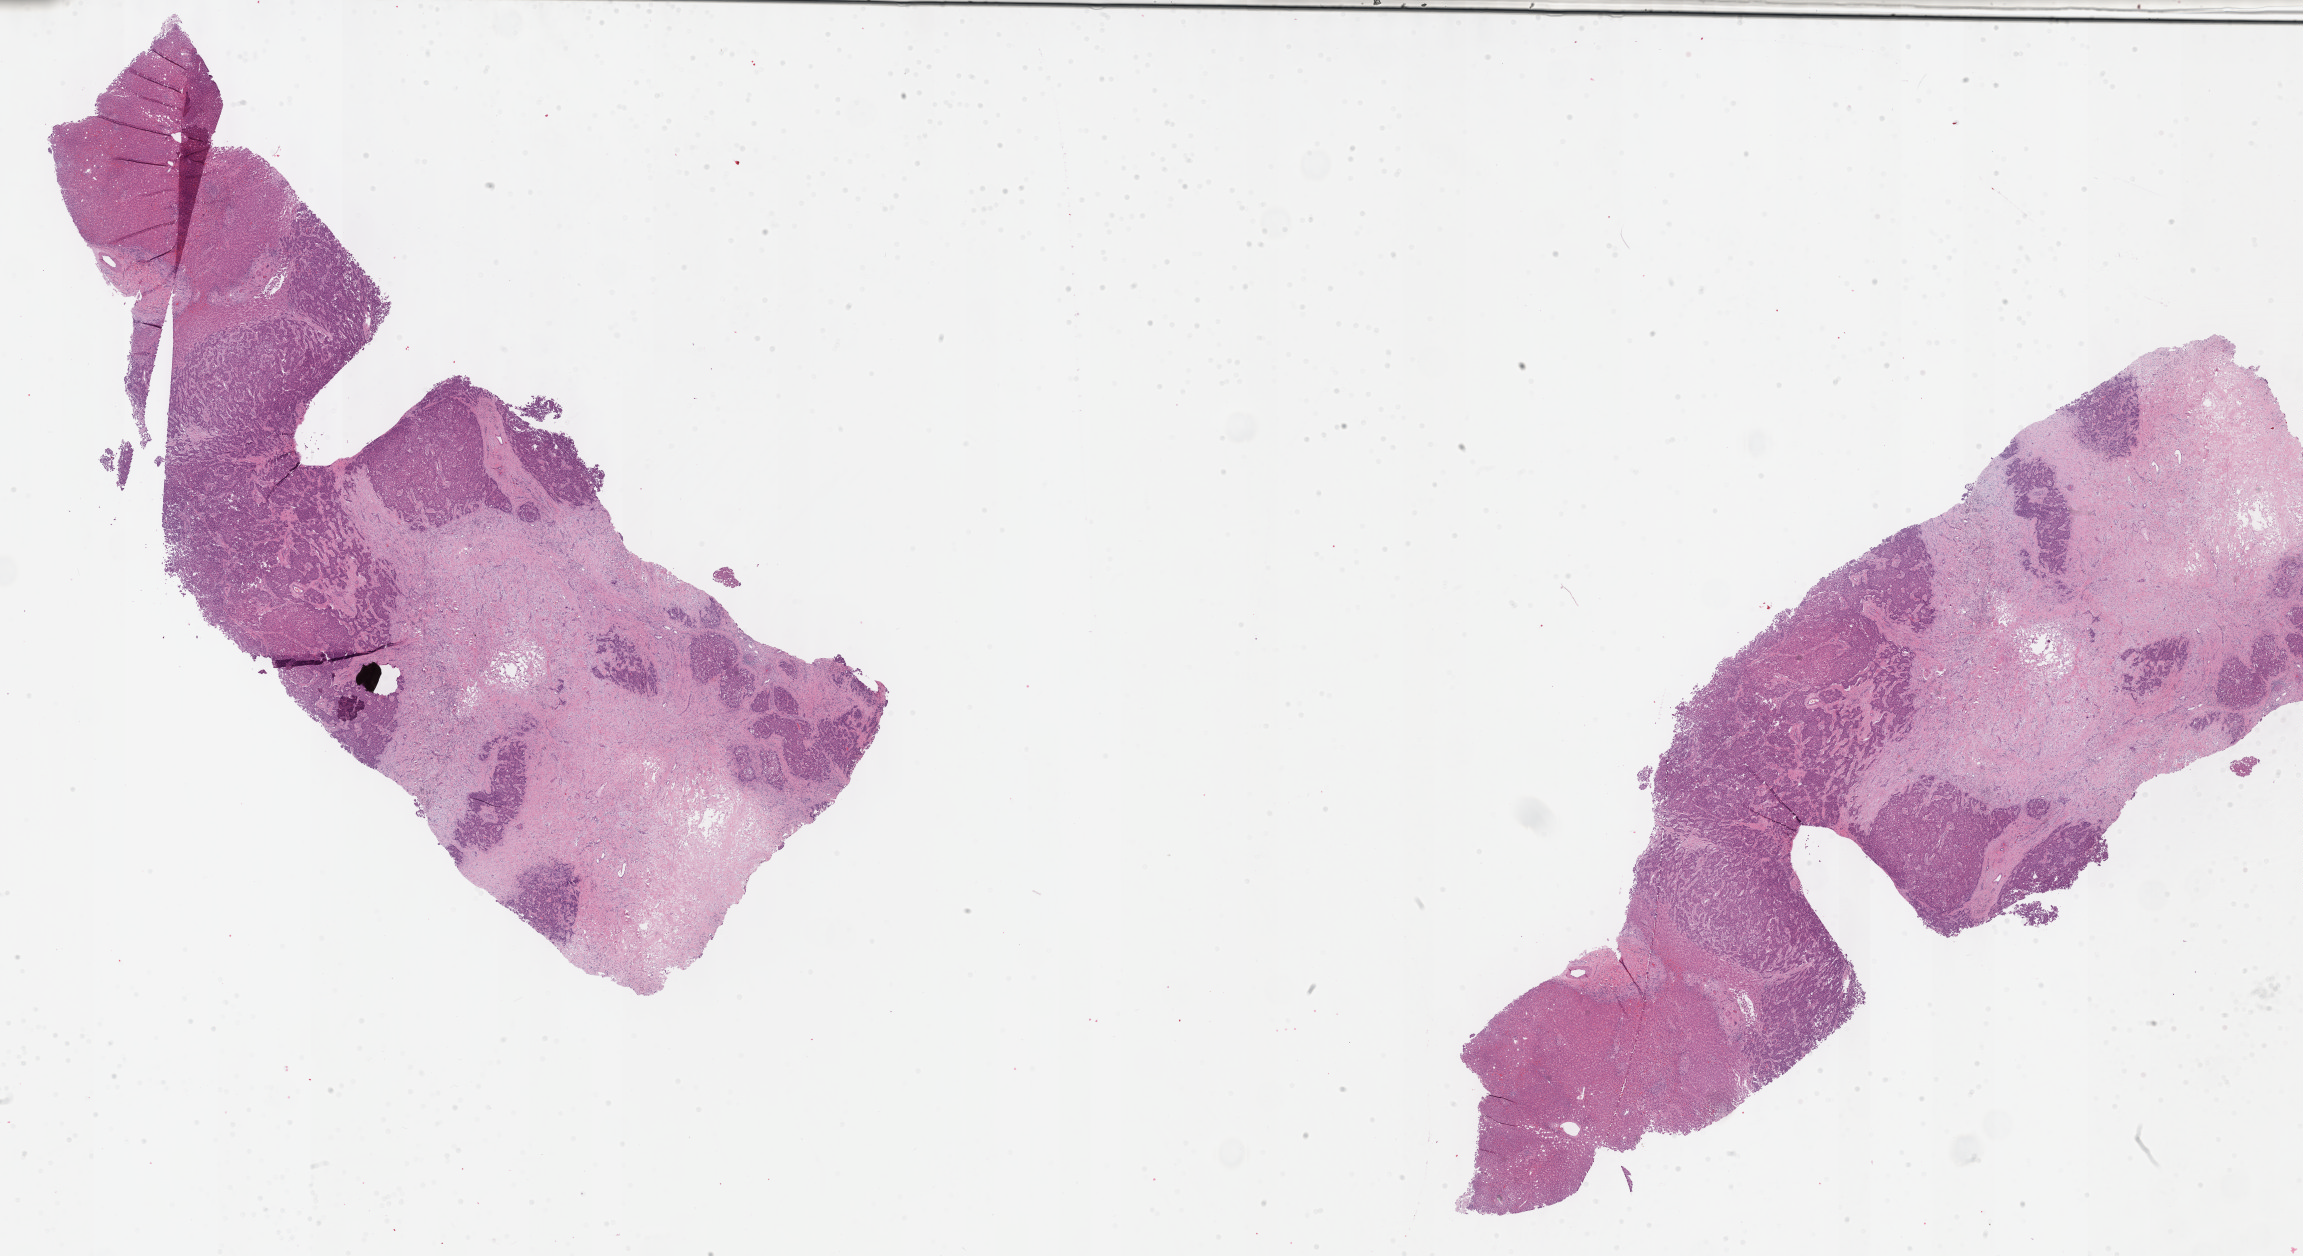
Digitized Hematoxylin and eosin (H&E) stained tissue section (whole slide) — low-resolution overview of the scanned area, about 37.2 x 20.3 mm (slide scanned at 40x); formalin-fixed paraffin-embedded (FFPE) diagnostic section; primary tumour sample from the liver. Patient: male, age at initial diagnosis 68 years.
Diagnosis: Hepatocellular carcinoma, NOS.